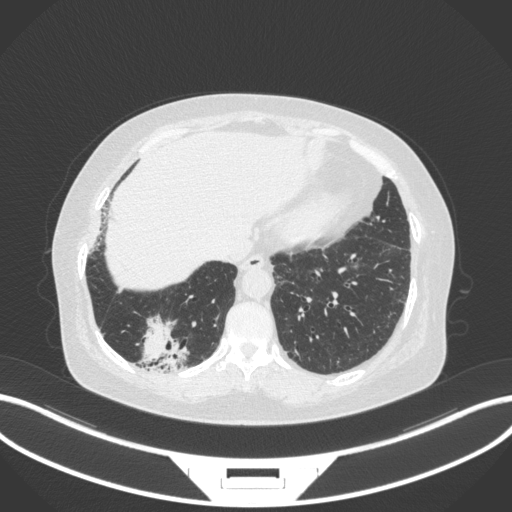
Chest CT, one axial slice; position 39 of 303 along the scan axis; reconstruction kernel B31f; 120 kVp; lung window (W 1500 / L -600 HU); 1 mm slice thickness; 512 × 512 image matrix, field of view 400 × 400 mm. Patient: female, 65 years. Case-level facts recorded for this patient, not image findings: clinical TNM (as recorded): T2b N1 M0; histopathological grade: G1.
Annotated regions visible in this slice (bounding box drawn by a radiologist):
- lung tumour (recorded histology: adenocarcinoma): bounding box (x1, y1, x2, y2) in pixels: (133, 314, 193, 373)